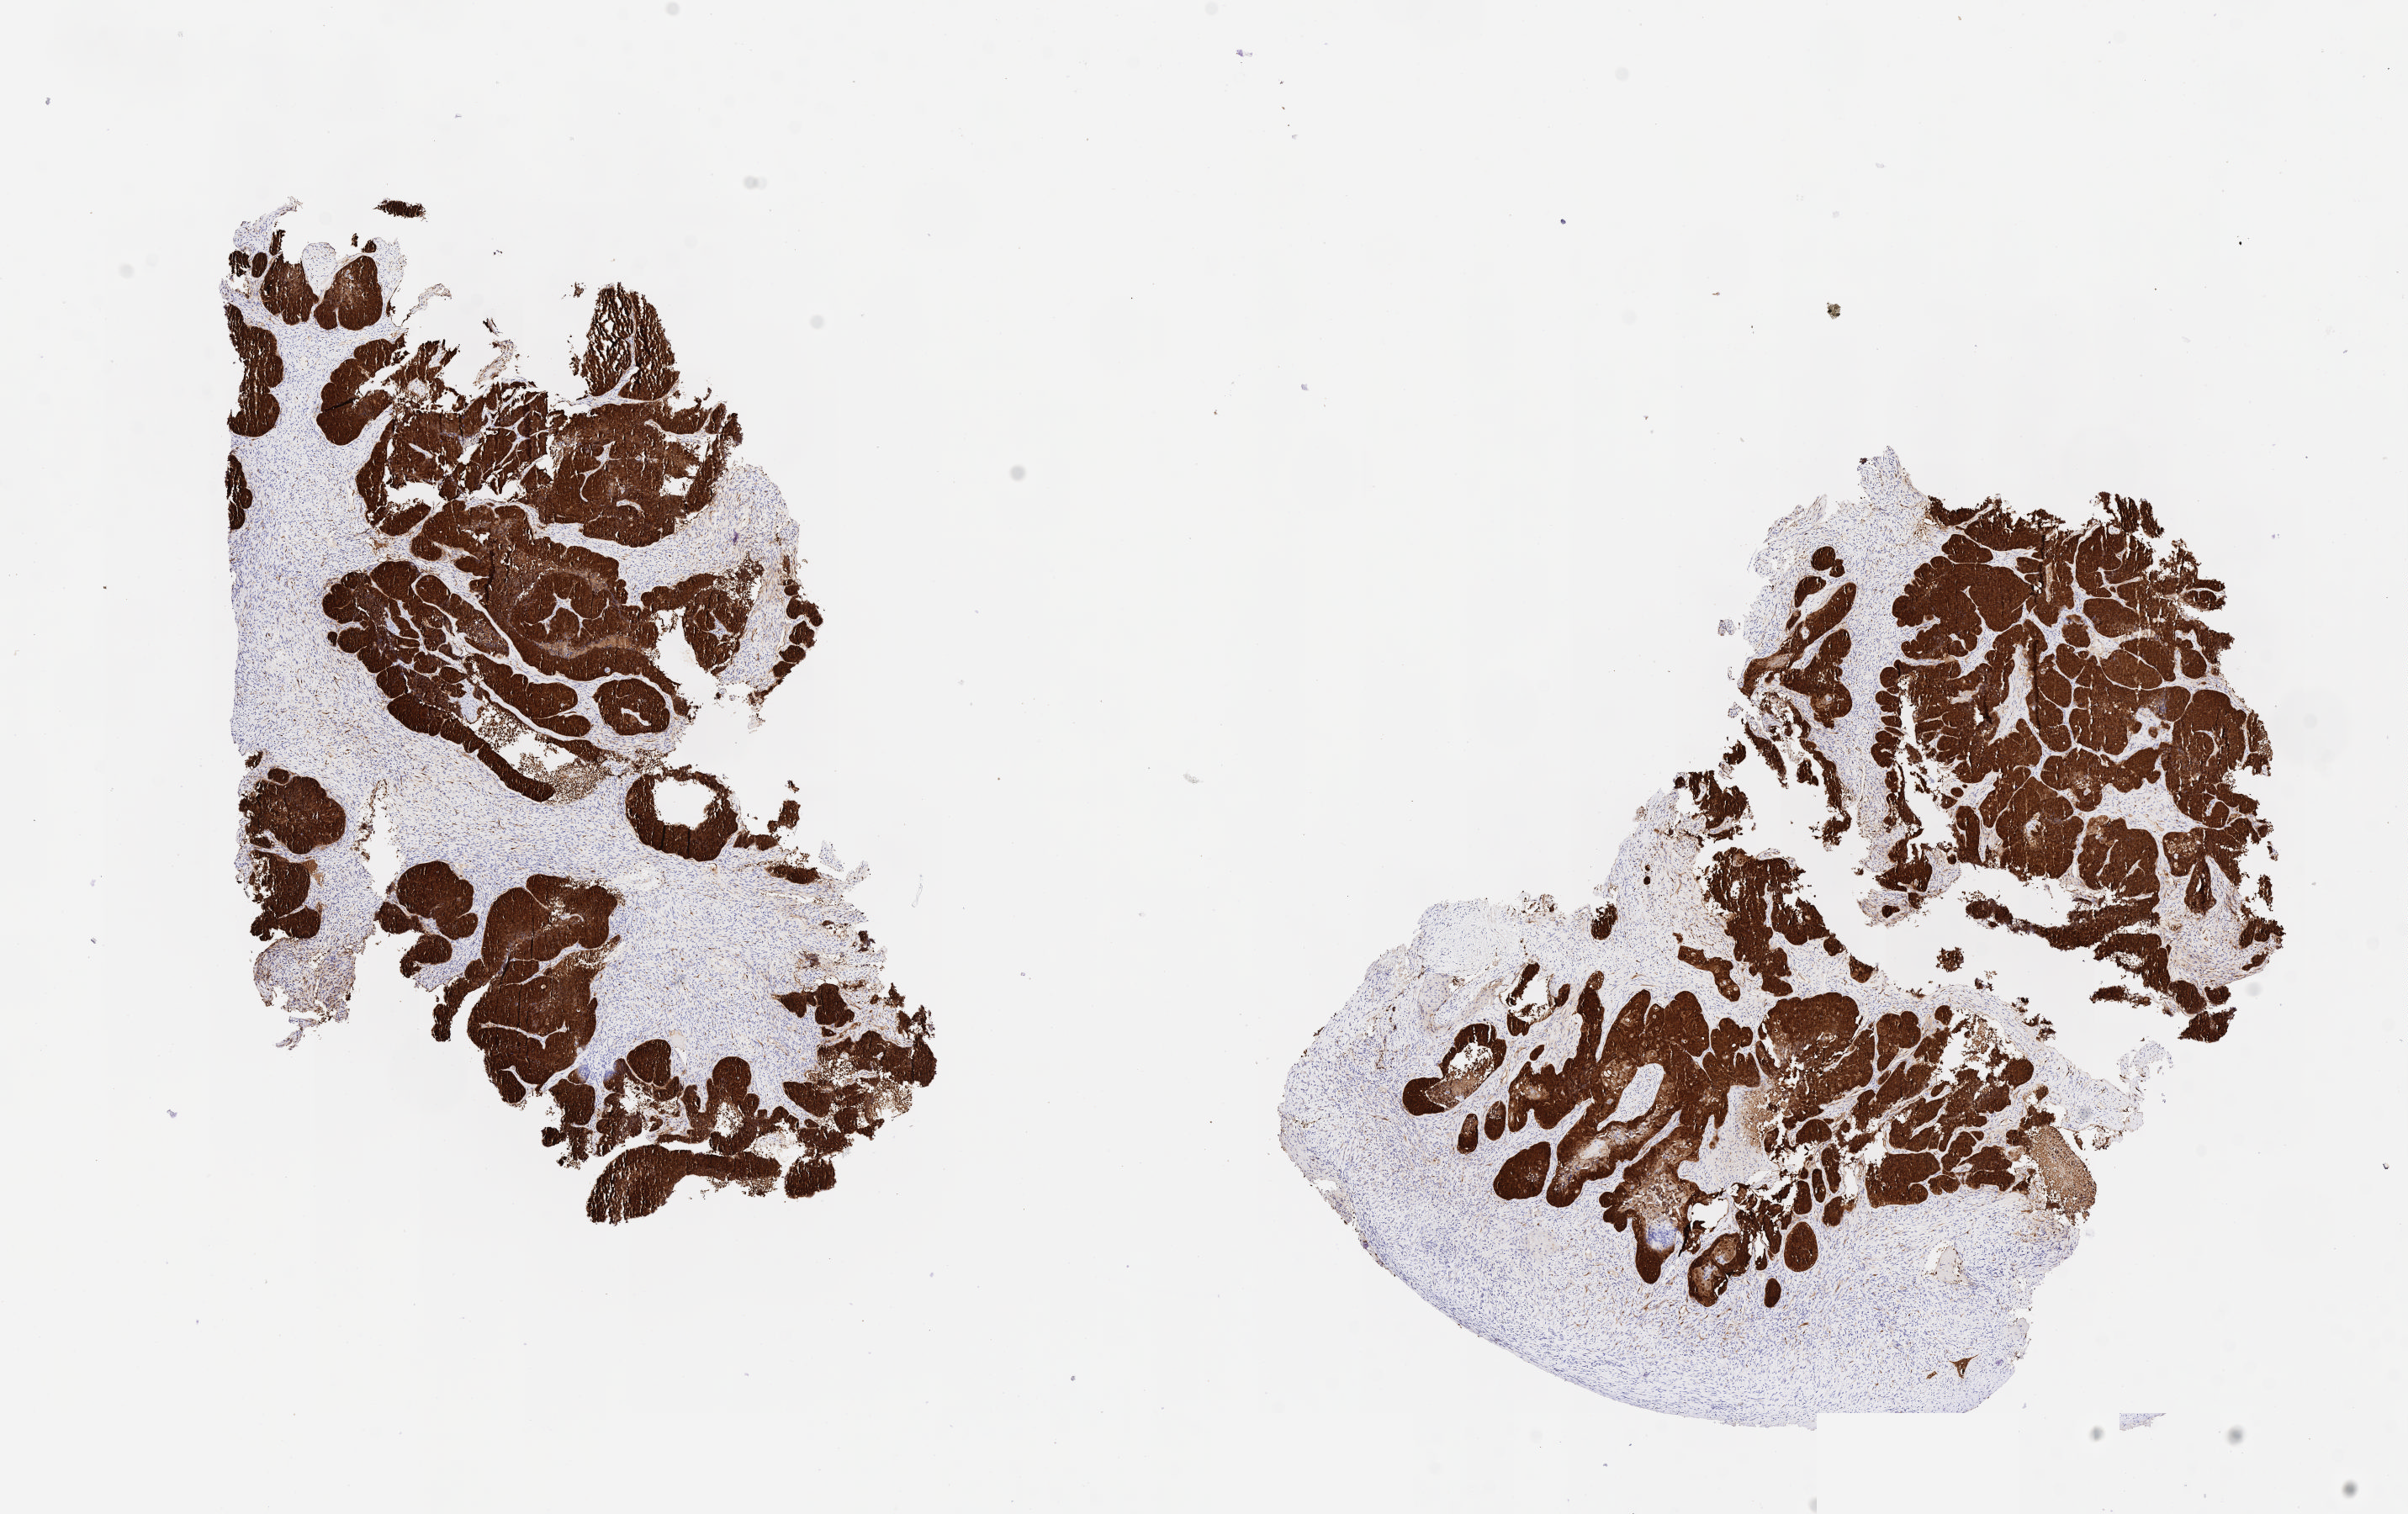
Whole-slide image, immunohistochemical stain for p16 (p16INK4a), a low-resolution overview of the entire scanned area, about 11.6 x 7.3 mm, specimen: tumor tissue, anatomic site: cervix. Patient: female, aged 38.
Histologic diagnosis: Squamous cell carcinoma, large cell, nonkeratinizing, NOS.